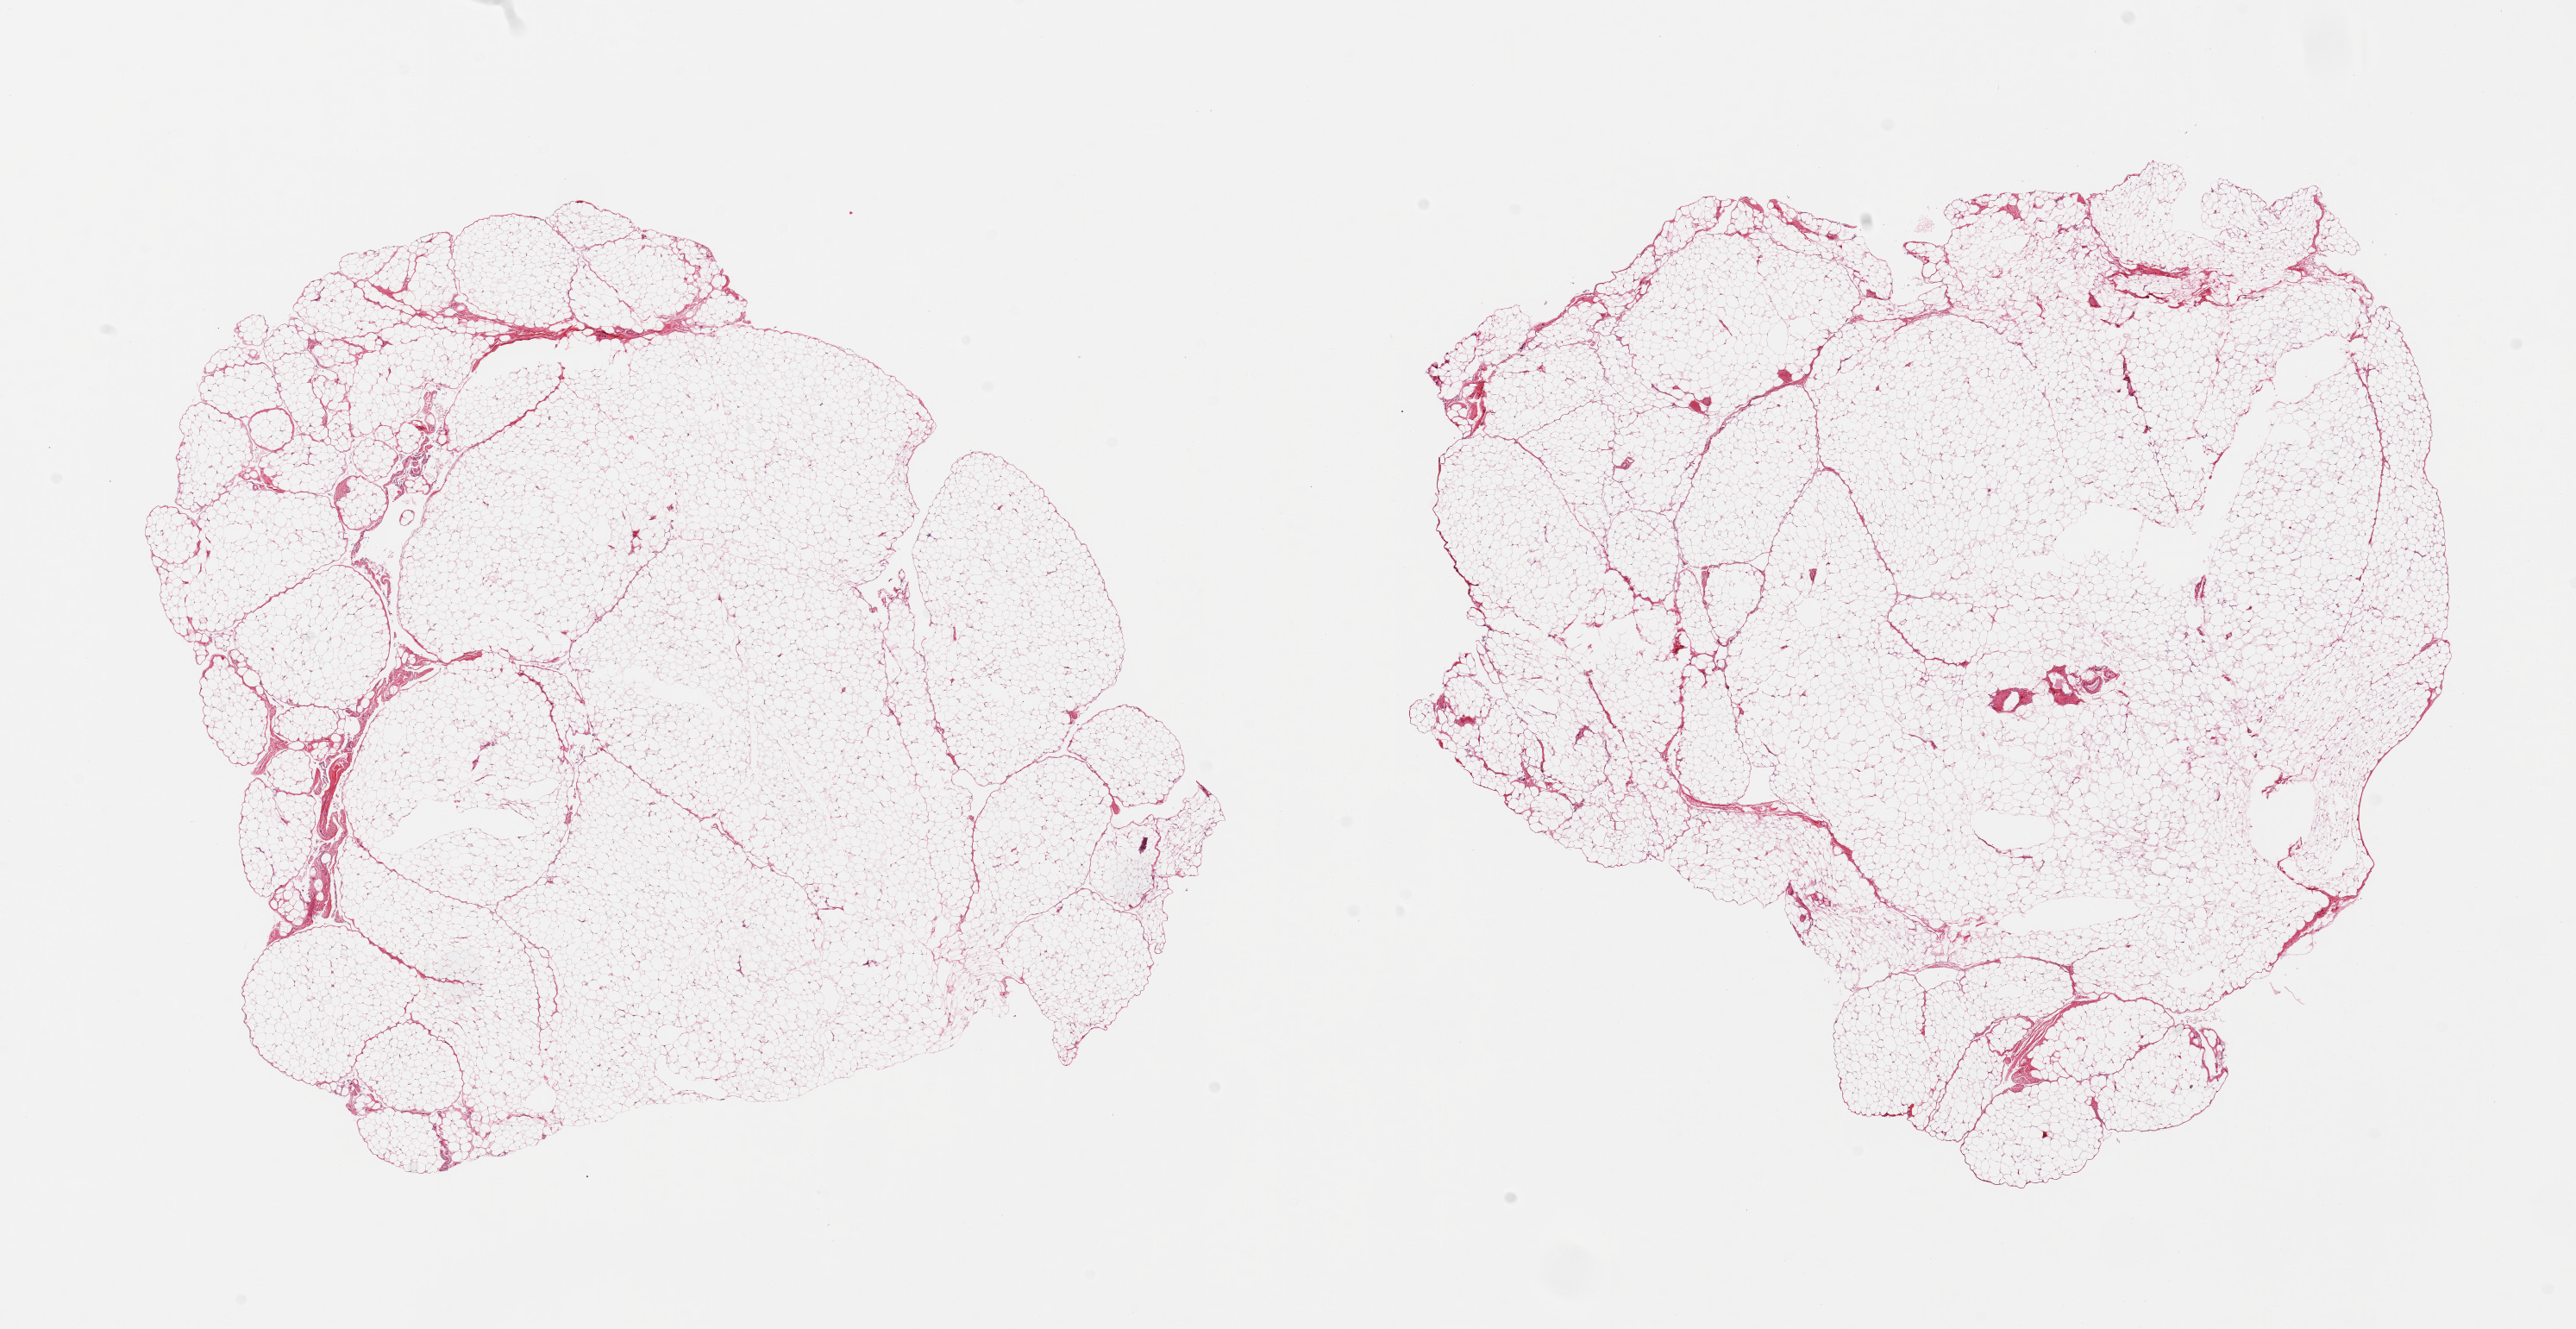
Digitized haematoxylin and eosin-stained section, brightfield — whole scanned area (about 23.6 x 12.2 mm, acquisition: 20x scan) shown as a low-resolution overview, PAXgene-fixed, paraffin-embedded tissue, target tissue: omentum, donor tissue sample. Female donor.
Pathologist's review note for this sample: 2 pieces; minimal fibrous content.